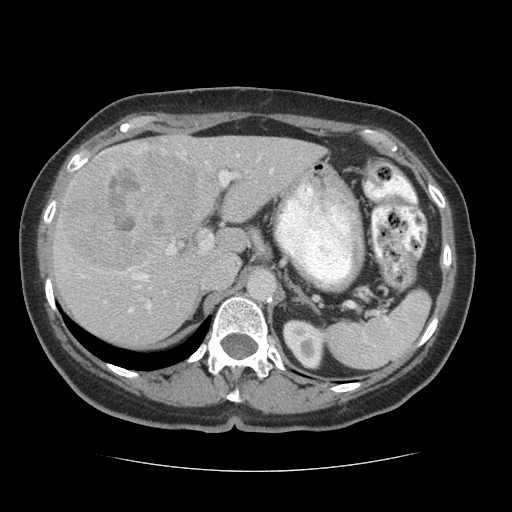
Contrast-enhanced abdominal CT (liver protocol), one axial slice. Slice 41 of 75 in the series (ordered by position). Reconstruction kernel STANDARD. Soft-tissue window (W 400 / L 40 HU). 2.5 mm slice thickness. 512 × 512 image matrix, field of view 360 × 360 mm. Case-level facts recorded for this patient, not image findings: diagnosis: hepatocellular carcinoma (patient treated with transarterial chemoembolisation; whether this scan precedes or follows treatment is not stated here); TNM stage (as recorded): Stage-I; Child-Pugh class: A.
Structures marked on this image (semi-automatic segmentation, software-assisted and operator-edited):
- liver parenchyma outside the tumour (the mass and vessels are separate outlines, so this box may not span the whole liver): bounding box <52,134,323,346> (left, top, right, bottom; pixels)
- mass: <61,148,197,272>
- liver vessels: <76,144,274,313>